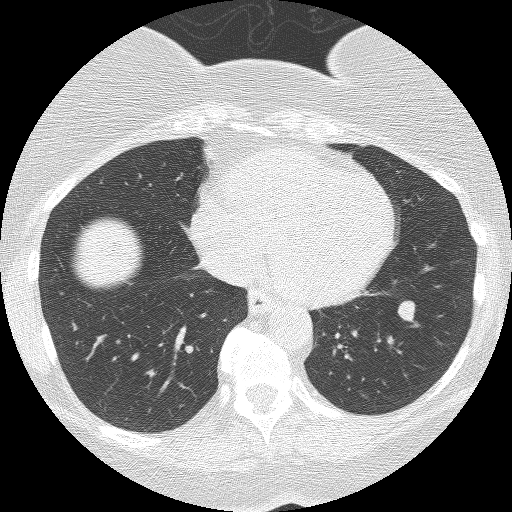
Axial slice from a low-dose chest CT screening exam; third annual screen; lung window (W 1500 / L -600 HU); 2.5 mm slice thickness; lung (sharp) reconstruction kernel (BONE). Female participant, aged 55 years at enrolment.
- Expert-annotated lung lesion, box from (x=380, y=290) to (x=429, y=336) px.
- The screening reader recorded 3 non-calcified nodules or masses ≥4 mm on this exam (right lower lobe, right lower lobe, left lower lobe); which of them this box marks is not recorded.
- Participant outcome: lung cancer diagnosed 356 days after this screen — carcinoid tumor, NOS, left lower lobe, carcinoid, stage not assessed, 10 mm at pathology.